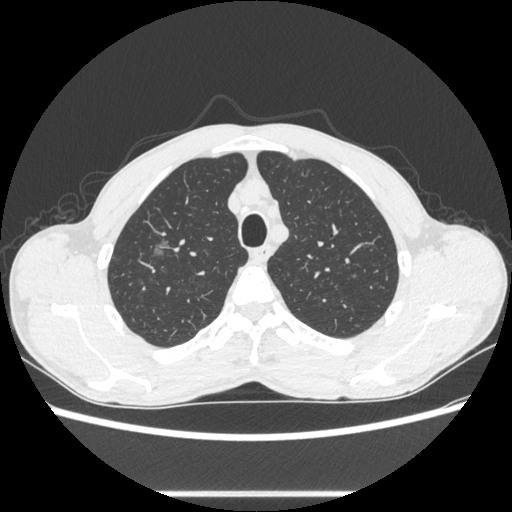
Chest CT, one axial slice; position 476 of 600 along the scan axis; reconstruction kernel STANDARD; lung window (W 1500 / L -600 HU); 0.62 mm slice thickness; 512 × 512 image matrix, field of view 357 × 357 mm. Male patient, age 54 years. Case-level facts recorded for this patient, not image findings: clinical TNM (as recorded): T1a N0 M0.
Structures marked on this image (rectangle marked by the reading radiologist):
- lung tumour (recorded histology: adenocarcinoma): box from (x=146, y=236) to (x=177, y=260) px